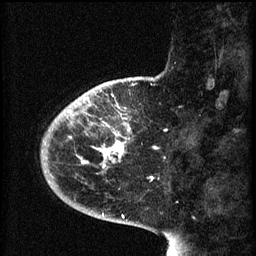
Breast MRI (dynamic contrast-enhanced), one sagittal slice; slice 14 of 60 in the series (ordered by position); 3 images stored at this slice position (order not interpretable as contrast timing); 1.5 T; TE 4.2 ms, TR 8.1 ms; 2 mm slice thickness; 256 × 256 image matrix. Female patient, age 44 years.
Annotated regions visible in this slice (semi-automatically segmented with operator editing):
- analysis volume of interest (the breast-tissue region the enhancement analysis was run in; not a lesion): bounding box (x1, y1, x2, y2) in pixels: (59, 110, 134, 167)
- tumour enhancement mask (voxels above the 70 % enhancement threshold inside the analysis volume of interest): (67, 110, 126, 167)